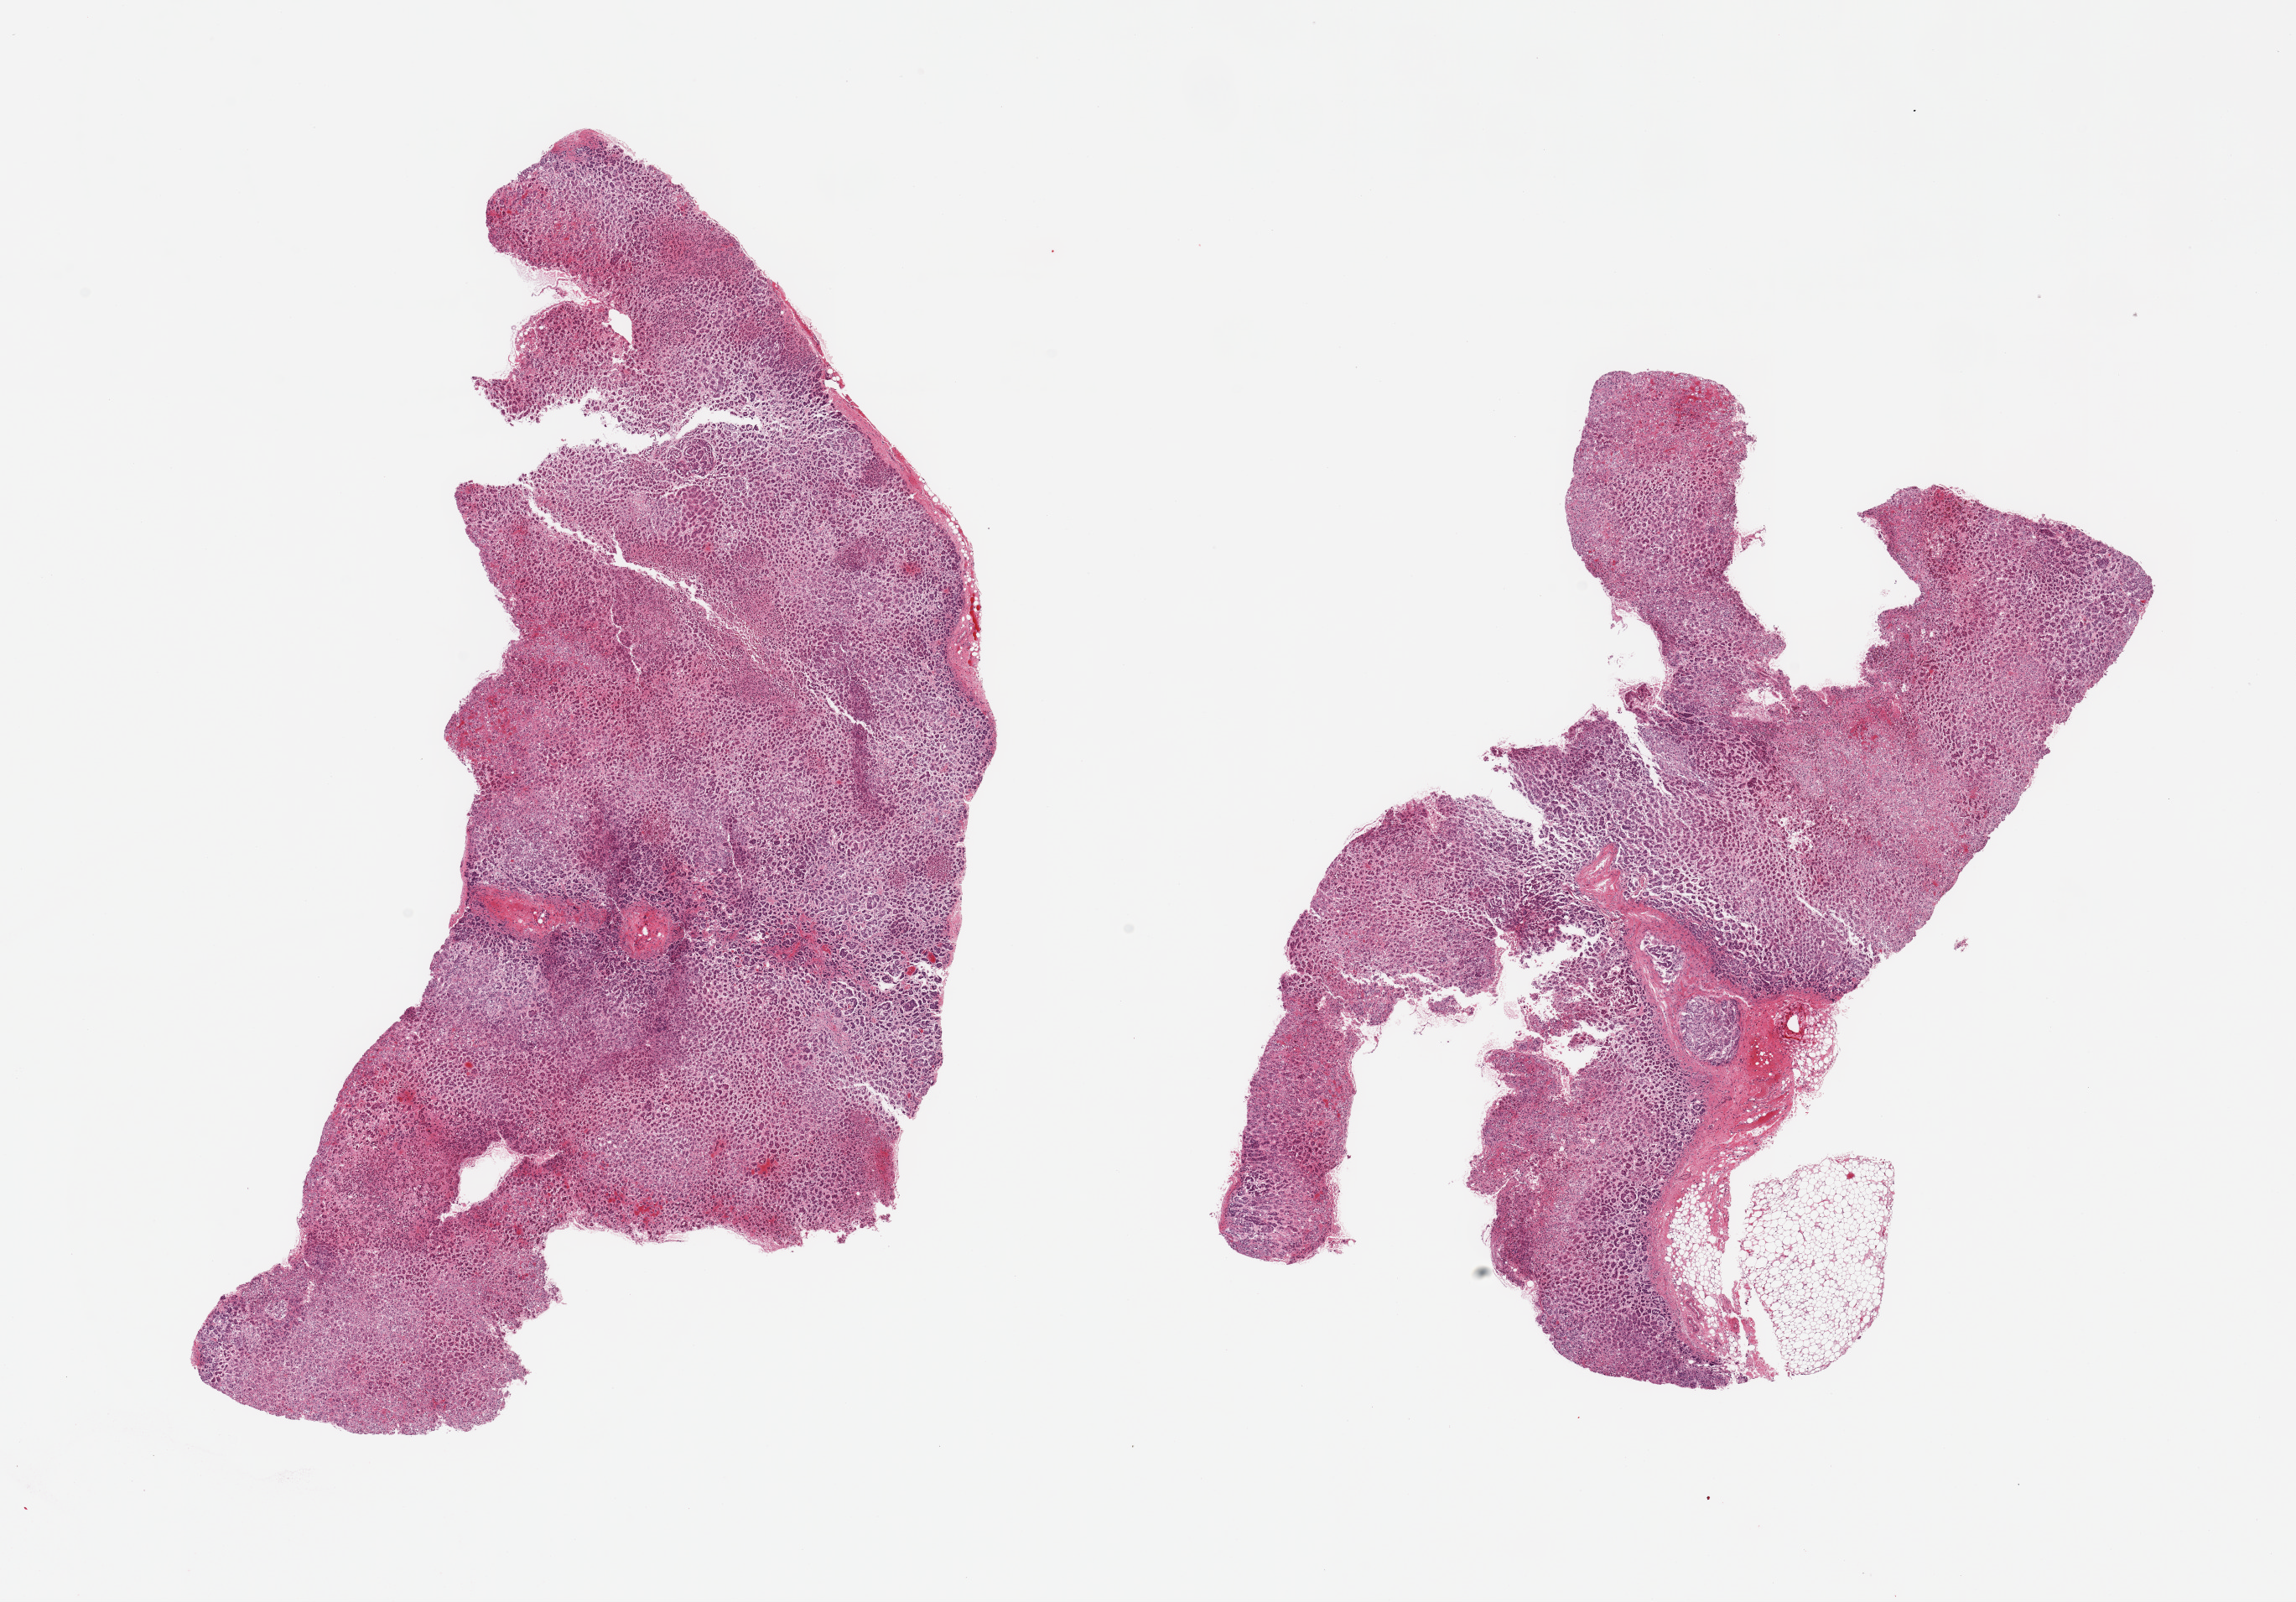
Haematoxylin and eosin whole-slide image, brightfield — shown as a low-resolution overview of the whole scanned area (about 21.7 x 15.1 mm, from a 20x scan). PAXgene-fixed, paraffin-embedded tissue. Sampled site (target tissue): adrenal gland. Donor tissue sample. Donor: female.
Reviewer comment on this tissue sample: 2 pieces; well trimmed except for a 1.7mm of external nodule of fat.